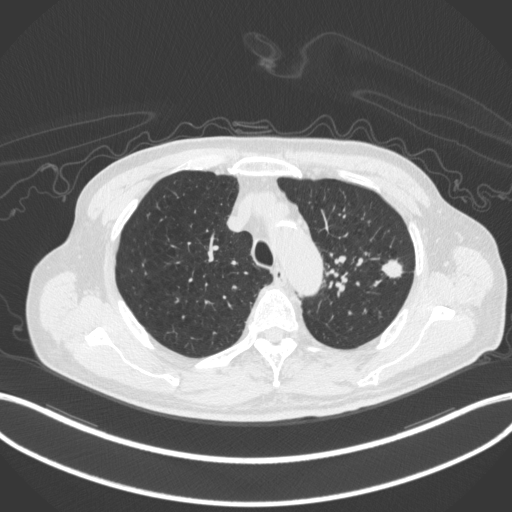
Chest CT, one axial slice; slice 343 of 420 in the series (ordered by position); reconstruction kernel B31f; 120 kVp; lung window (W 1500 / L -600 HU); 1 mm slice thickness; 512 × 512 image matrix, field of view 400 × 400 mm. Male patient, age 77 years. Case-level facts recorded for this patient, not image findings: clinical TNM (as recorded): T3 N1 M0.
Outlined on this slice (bounding box drawn by a radiologist):
- lung tumour (recorded histology: adenocarcinoma): bounding box (x1, y1, x2, y2) in pixels: (380, 253, 406, 282)